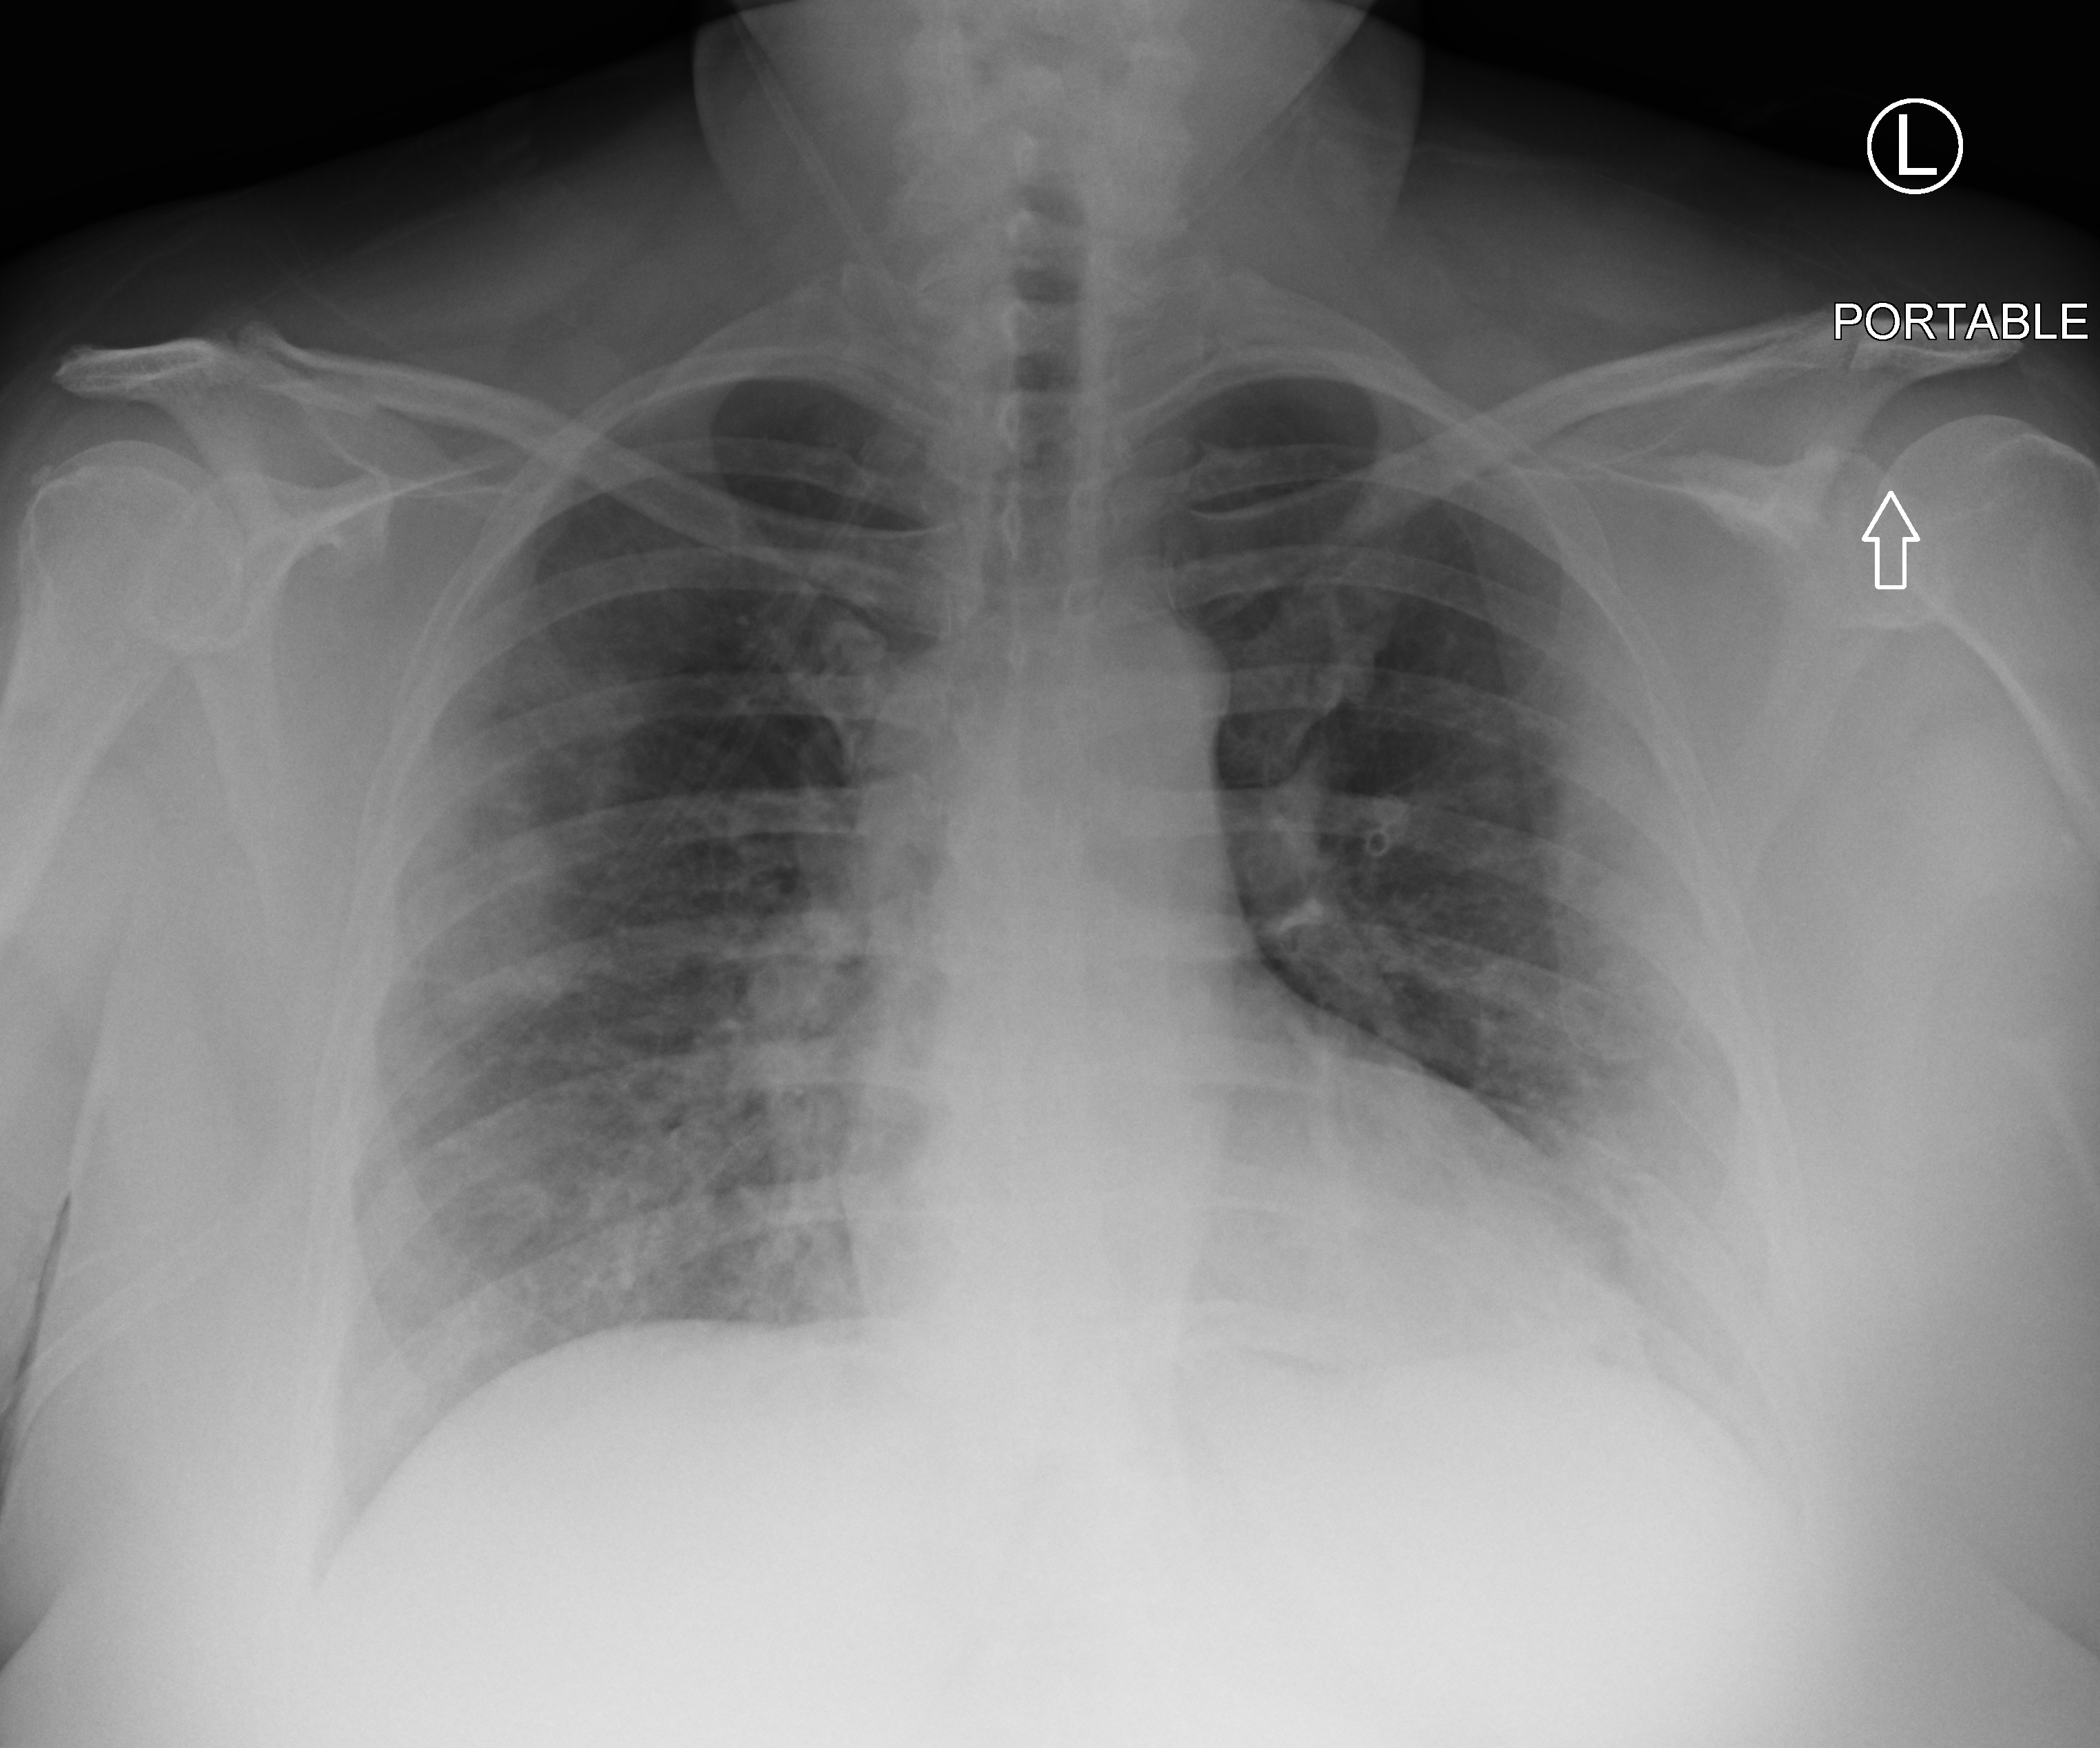
Bedside chest radiograph (computed radiography); anteroposterior (AP) projection. Female patient hospitalised with COVID-19, age 18–59 years.
From the hospital-stay record, not from the radiograph (when in the stay this image was taken is not recorded): mechanically ventilated during this hospital stay: no; admitted to intensive care during this hospital stay: no.